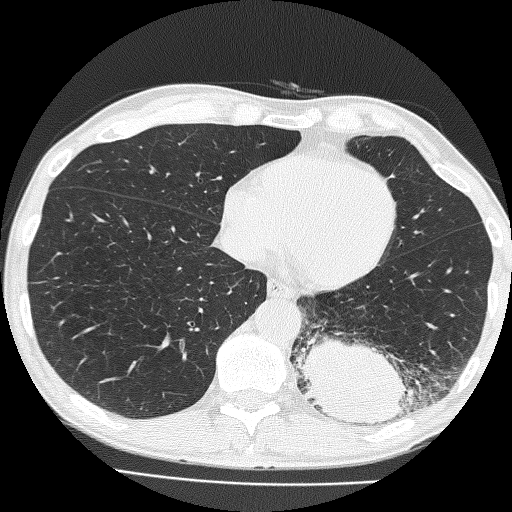
Low-dose screening chest CT, one axial slice; position 55 of 160 along the scan axis; lung window (W 1500 / L -600 HU); 512 × 512 image matrix, field of view 324 × 324 mm.
Structures marked on this image (manually delineated by an expert):
- lesion 1 (tumor, lower lobe of left lung): box from (x=295, y=336) to (x=410, y=426) px